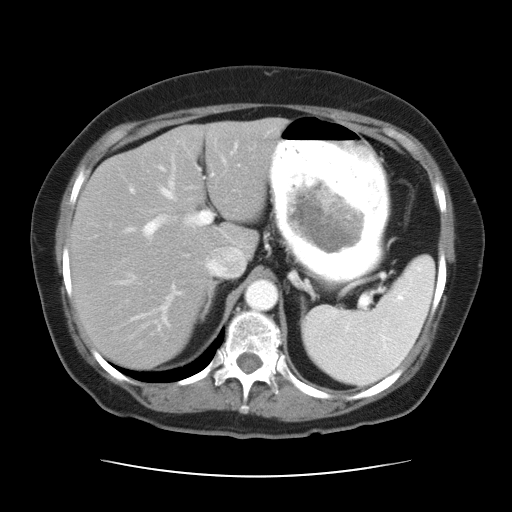
Contrast-enhanced abdominal CT, one axial slice; position 22 of 34 along the scan axis; reconstruction kernel STANDARD; 120 kVp; soft-tissue window (W 400 / L 40 HU); 512 × 512 image matrix. Female patient, age 65 years. From the clinical record (not read from this slice): diagnosis: colorectal cancer liver metastases, imaged before liver resection; multiple liver metastases: yes; largest metastasis: 2.2 cm; chemotherapy before resection: yes.
Outlined on this slice (manually delineated by an expert):
- hepatic veins: bounding box <119,156,245,284> (left, top, right, bottom; pixels)
- liver: <71,121,279,366>
- planned liver remnant (the part of the liver to remain after resection): <71,121,279,357>
- portal vein (with intrahepatic branches): <124,145,238,327>